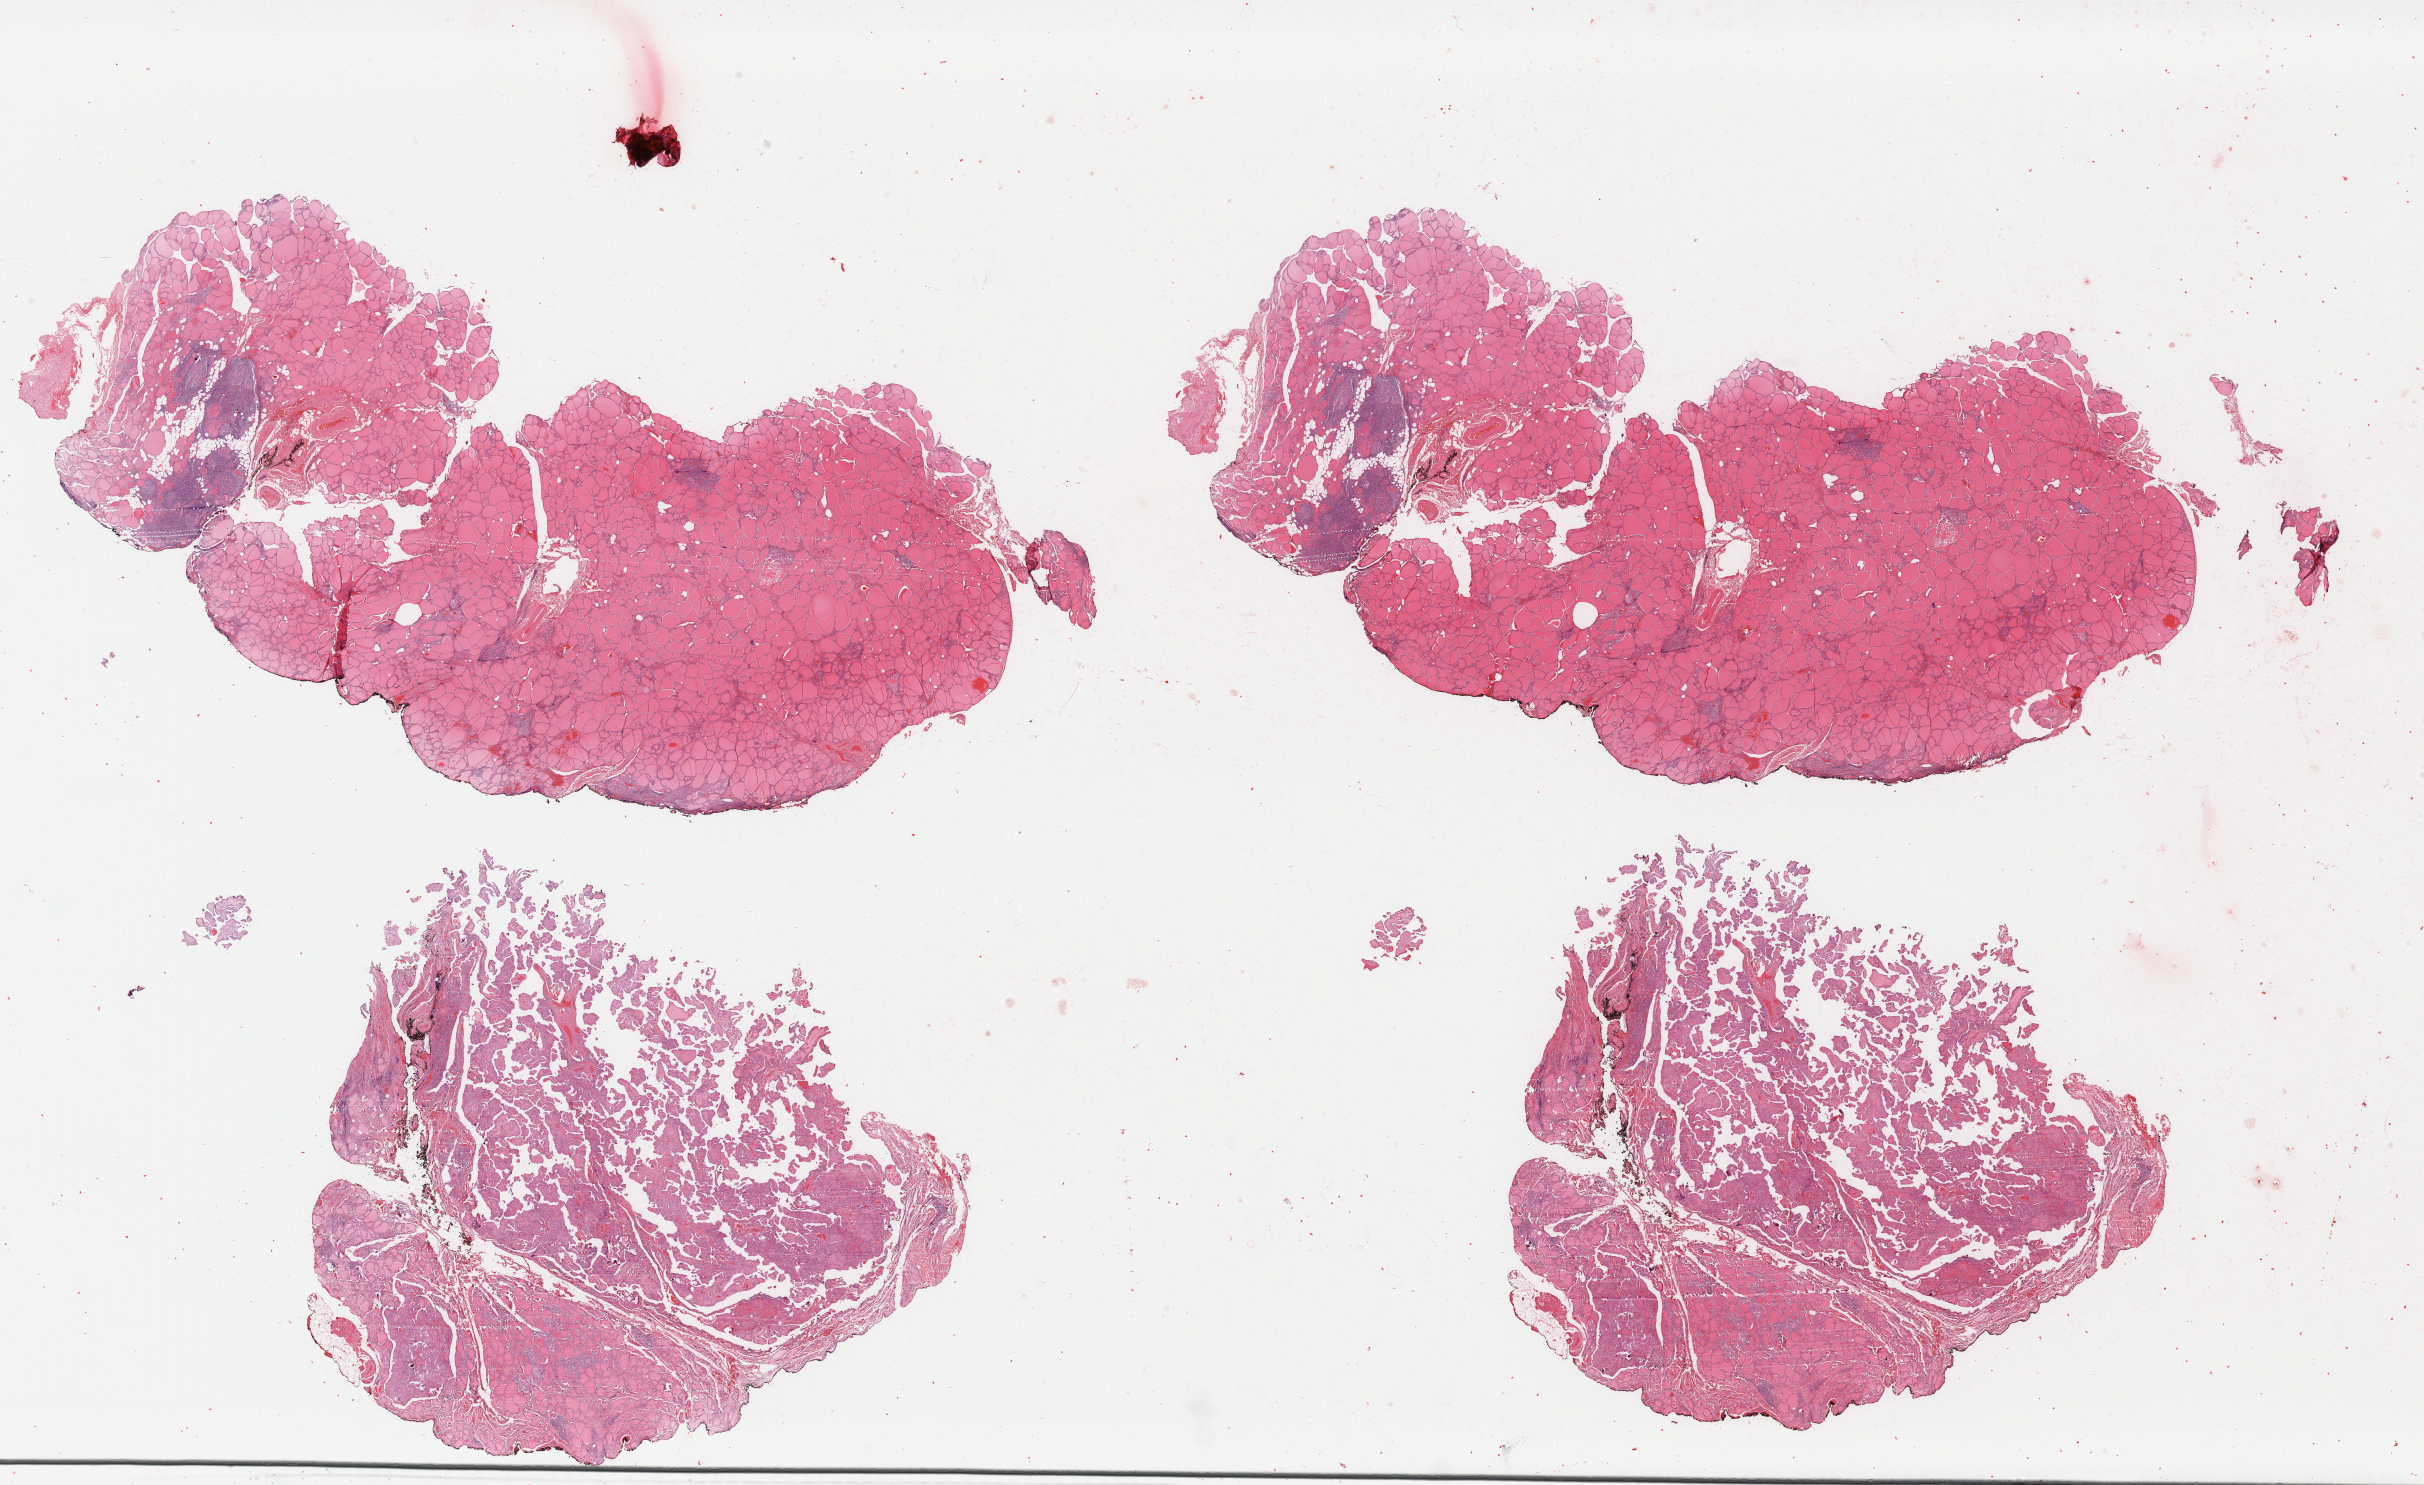
Whole-slide histology image, Hematoxylin and eosin (H&E) stained, a low-resolution overview of the entire scanned area, about 38.5 x 23.6 mm. FFPE section. Primary tumour sample from the thyroid. Patient: female, age at initial diagnosis 34 years.
Laterality: left. AJCC pathologic stage: I. Lymph nodes positive (case pathology): 0 of 3 examined. Pathologic diagnosis: Papillary adenocarcinoma, NOS (thyroid gland).